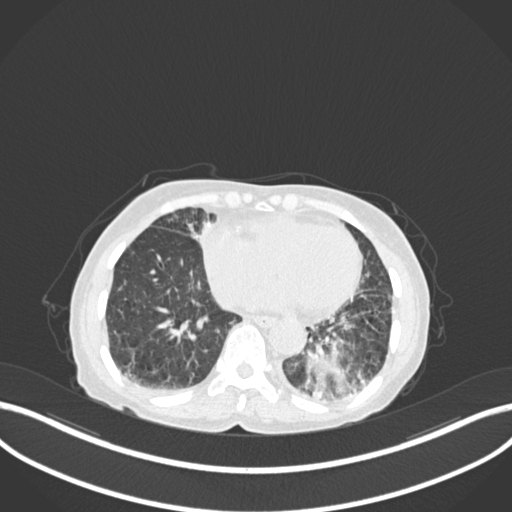
Chest CT, one axial slice; slice 36 of 233 in the series (ordered by position); 120 kVp; lung window (W 1500 / L -600 HU); 1 mm slice thickness; 512 × 512 image matrix, field of view 400 × 400 mm. Female patient, age 78 years. From the clinical record (not read from this slice): clinical TNM (as recorded): T3 N0 M1.
Annotated regions visible in this slice (rectangle marked by the reading radiologist):
- lung tumour (recorded histology: squamous cell carcinoma): bounding box (x1, y1, x2, y2) in pixels: (306, 341, 368, 402)